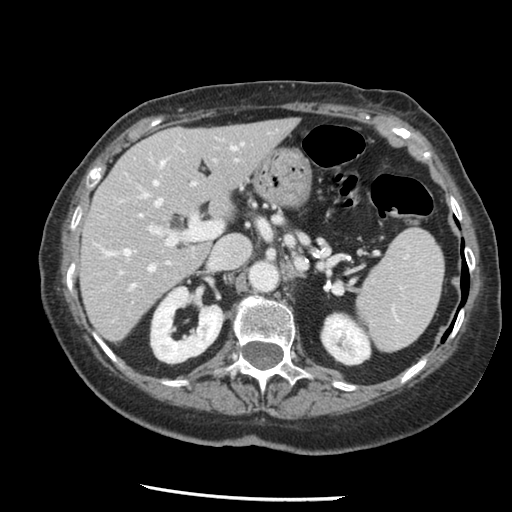
Contrast-enhanced abdominal CT, one axial slice; slice 81 of 148 in the series (ordered by position); reconstruction kernel STANDARD; intravenous contrast given; soft-tissue window (W 400 / L 40 HU); 2.5 mm slice thickness; 512 × 512 image matrix. Female patient, age 85 years. From the clinical record (not read from this slice): diagnosis: colorectal cancer liver metastases, imaged before liver resection; multiple liver metastases: no; largest metastasis: 0.9 cm; disease in both lobes: no.
Structures marked on this image (outlined manually by an expert reader):
- hepatic veins: bounding box (x1, y1, x2, y2) in pixels: (103, 142, 185, 289)
- liver: (81, 119, 297, 341)
- planned liver remnant (the part of the liver to remain after resection): (81, 119, 297, 341)
- portal vein (with intrahepatic branches): (139, 140, 230, 246)